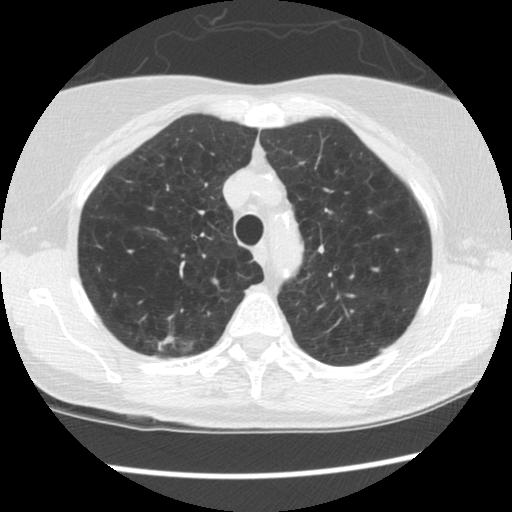
Low-dose screening chest CT, one axial slice. 120 kVp. Lung window (W 1500 / L -600 HU). 2.5 mm slice thickness. 512 × 512 image matrix, field of view 319 × 319 mm.
Outlined on this slice (expert manual segmentation):
- lesion 1 (tumor, upper lobe of right lung): bounding box [x1, y1, x2, y2] px = [158, 335, 175, 351]